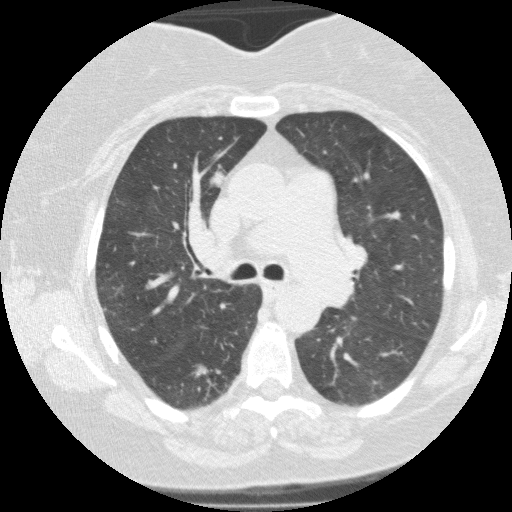
Low-dose screening chest CT, axial slice; third screening round (two years after baseline); lung window (W 1500 / L -600 HU); 2 mm slice thickness. Female participant, aged 62 years at enrolment. Current smoker at enrolment.
- Expert reader's lesion annotation, bounding box [x1, y1, x2, y2] px = [188, 155, 235, 201].
- The screening reader recorded 5 non-calcified nodules or masses ≥4 mm on this exam (right upper lobe, right lower lobe, right lower lobe, right lower lobe, right lower lobe); which of them this box marks is not recorded.
- Official screen result: positive, other.
- Later outcome: lung cancer diagnosed 76 days after this screen — adenocarcinoma, NOS, right upper lobe, poorly differentiated (G3), stage IB (AJCC 6th edition), 12 mm at pathology.